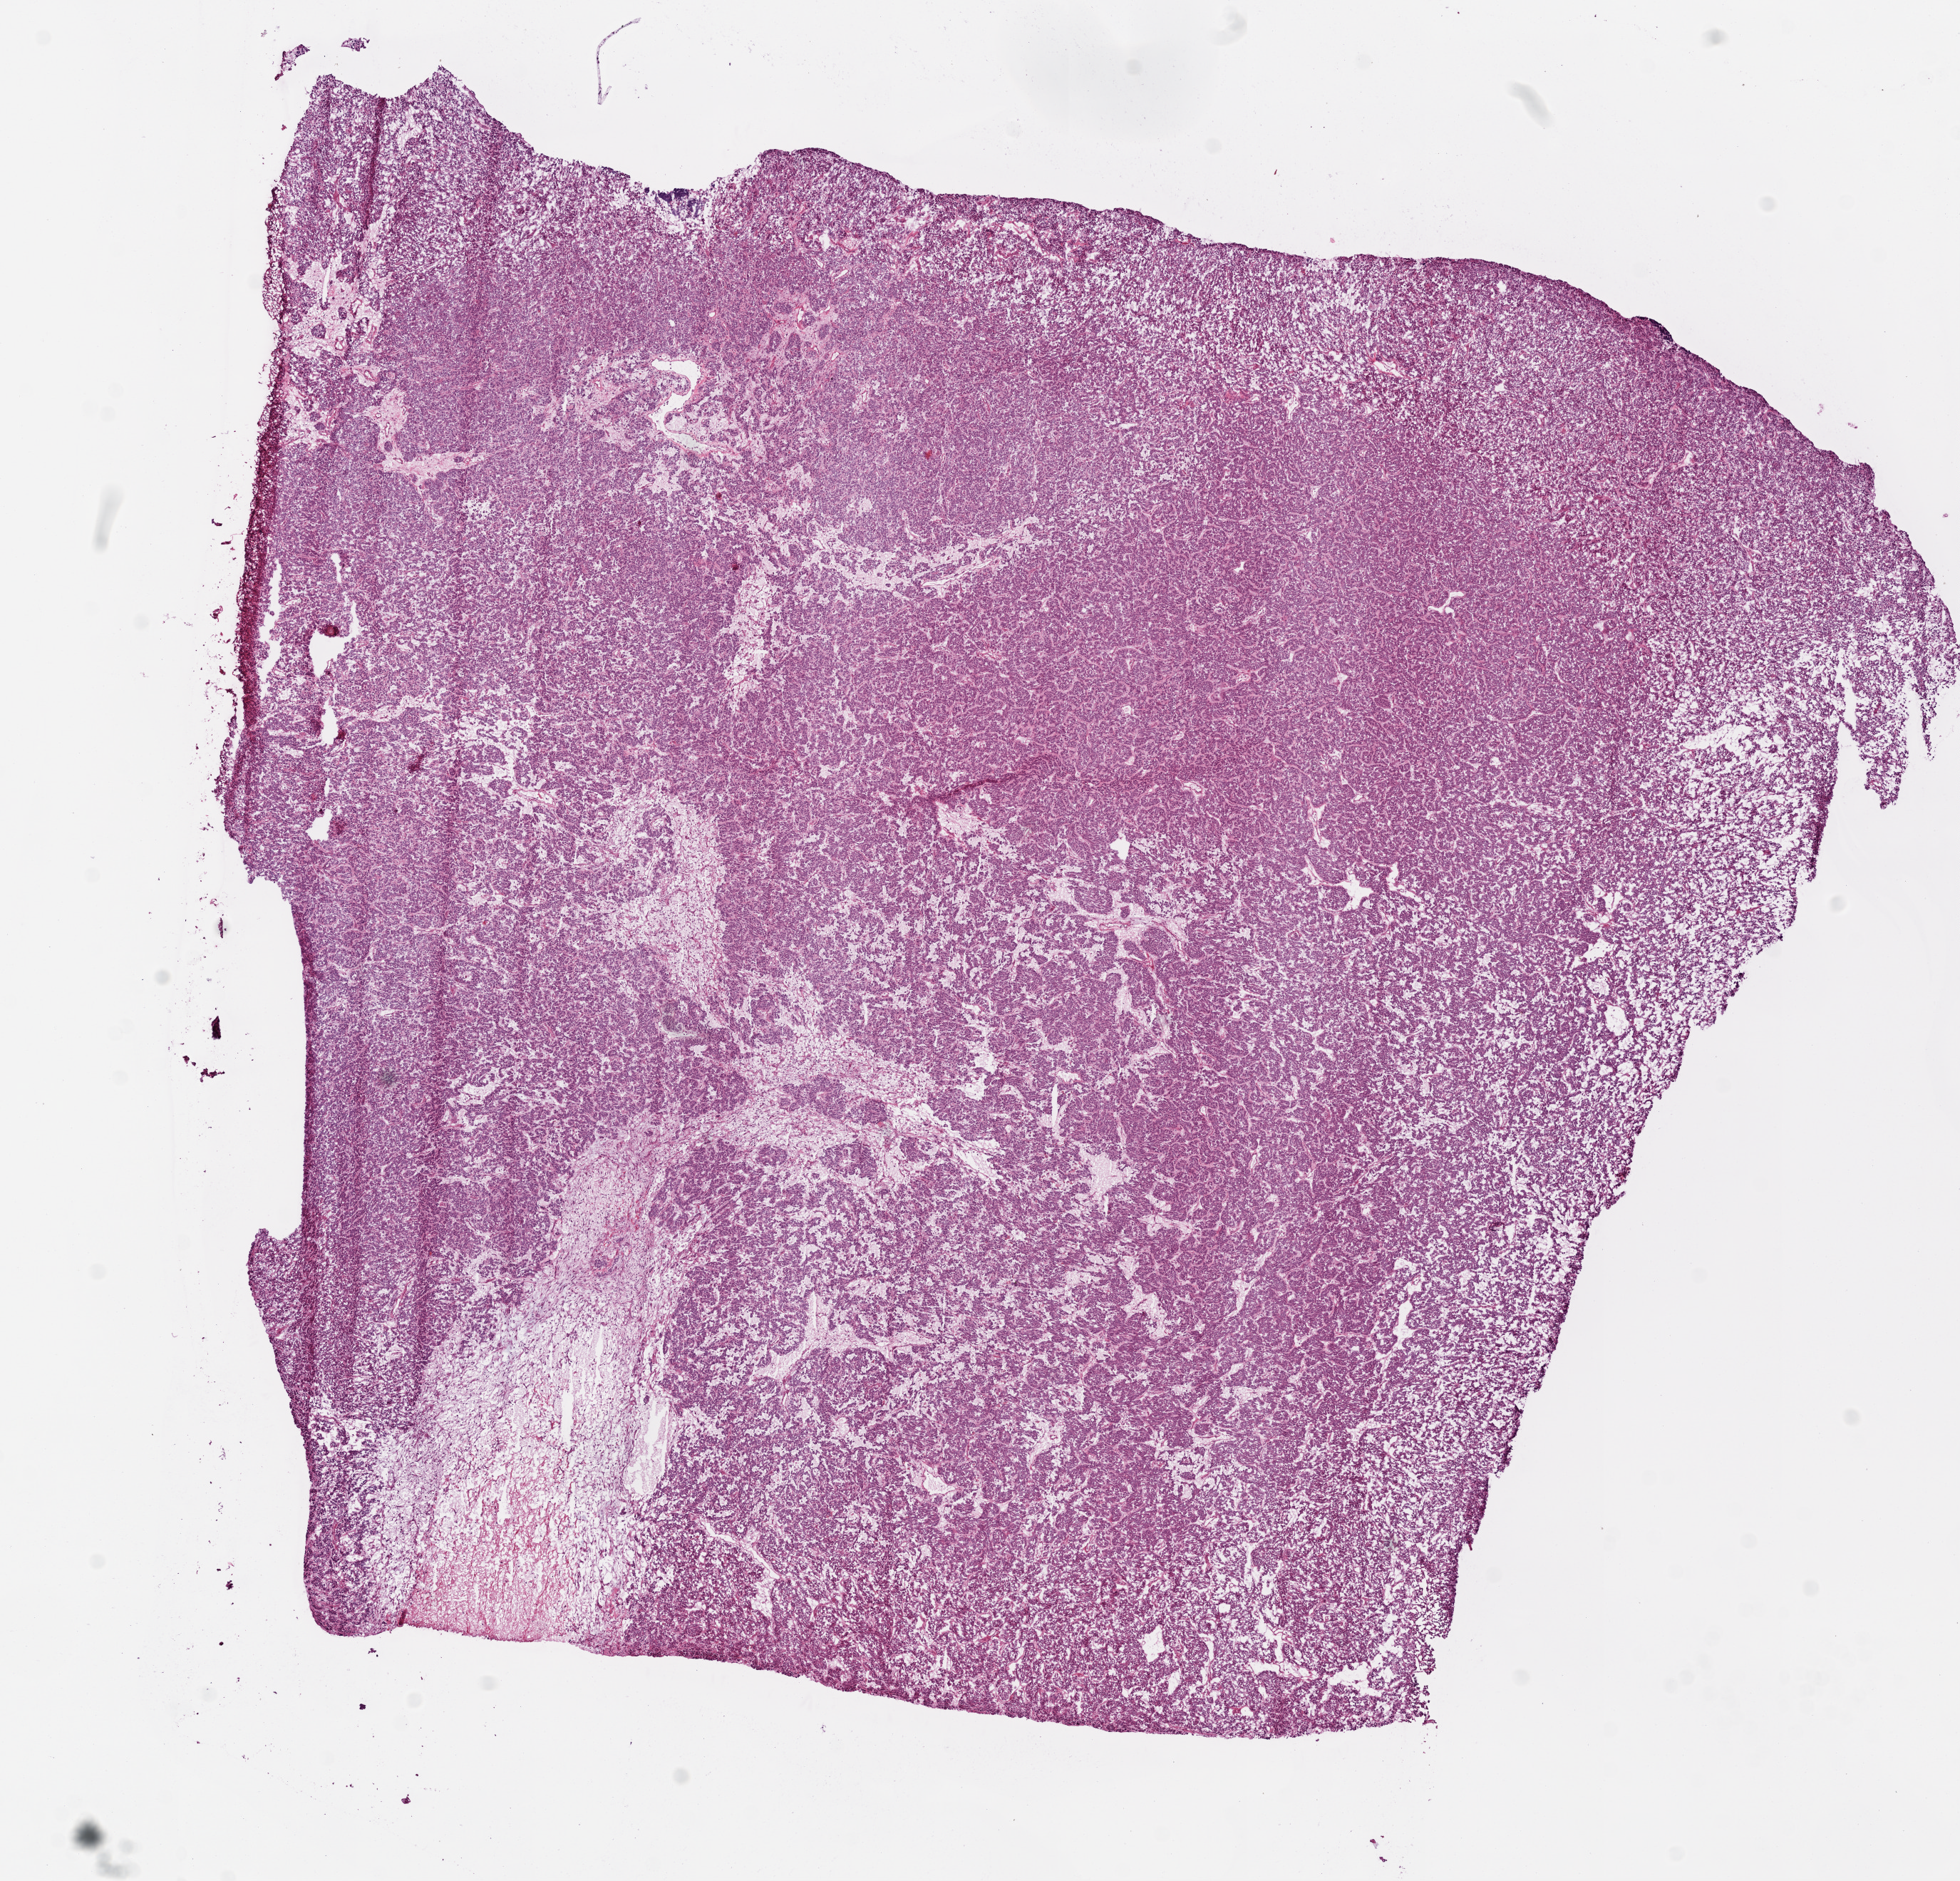
Digitized H&E-stained tissue section (whole slide) — low-resolution overview of the scanned area, about 11.0 x 10.6 mm, frozen section from the bottom of the tissue portion, sample: primary tumour, lung. Female, age 52 years at initial diagnosis. Slide review estimates, as recorded: tumour cells 85%, tumour nuclei 80%, normal cells 5%, stromal cells 10%, necrosis 0%.
AJCC pathologic stage: IA (7th edition). Pathologic diagnosis: Squamous cell carcinoma, NOS (middle lobe, lung).